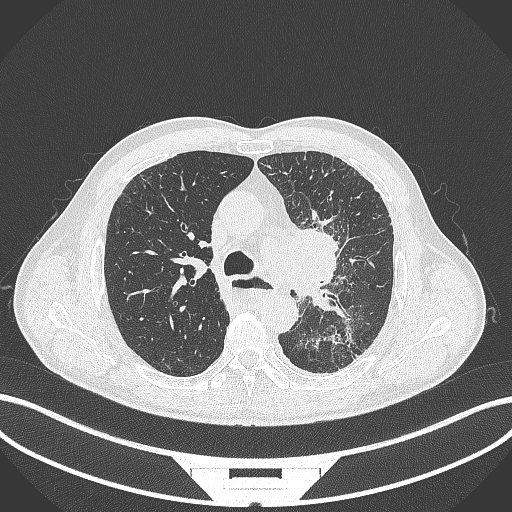
Chest CT, one axial slice; slice 260 of 411 in the series (ordered by position); reconstruction kernel B70f; 120 kVp; lung window (W 1500 / L -600 HU); 1 mm slice thickness; 512 × 512 image matrix, field of view 400 × 400 mm. Male patient, age 57 years. From the clinical record (not read from this slice): clinical TNM (as recorded): T2a N1 M0.
Annotated regions visible in this slice (bounding box drawn by a radiologist):
- lung tumour (recorded histology: squamous cell carcinoma): bounding box (x1, y1, x2, y2) in pixels: (291, 219, 342, 297)